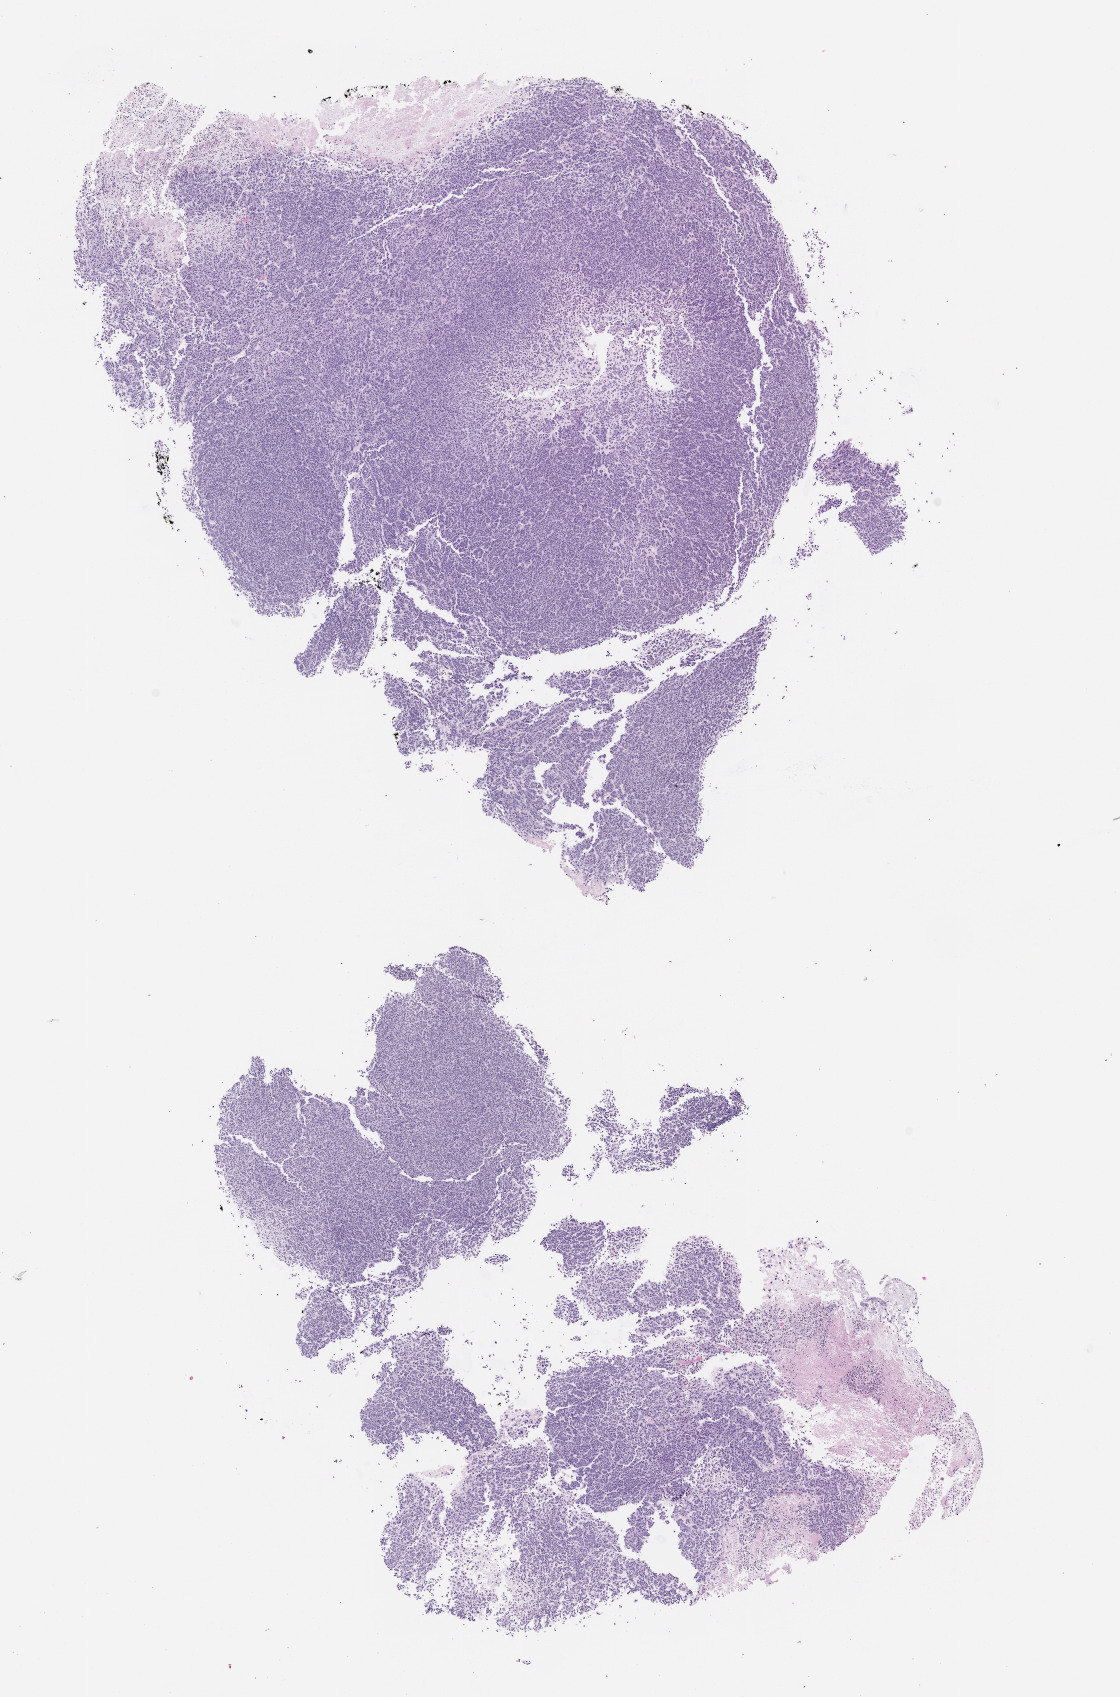
Whole-slide image, hematoxylin and eosin (H&E): patient-derived xenograft (human tumor grown in a mouse), passage 1, shown as a low-resolution overview of the whole scanned area (about 9.0 x 13.7 mm); formalin-fixed paraffin-embedded section; tumor site category: bladder.
- originating patient diagnosis: Urothelial Carcinoma